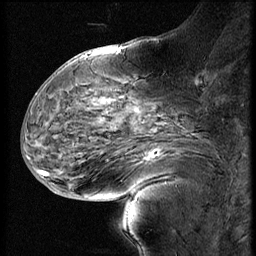
Breast MRI (dynamic contrast-enhanced), one sagittal slice; position 27 of 60 along the scan axis; 4 images stored at this slice position (order not interpretable as contrast timing); 1.5 T; TE 4.2 ms, TR 9 ms; 256 × 256 image matrix. Female patient, age 56 years. From the clinical record (not read from this slice): setting: breast cancer imaged before/during neoadjuvant chemotherapy; receptor status: HER2-positive.
Annotated regions visible in this slice (semi-automatically segmented with operator editing):
- analysis volume of interest (the breast-tissue region the enhancement analysis was run in; not a lesion): bounding box [x1, y1, x2, y2] px = [110, 138, 192, 201]
- tumour enhancement mask (voxels above the 140 % enhancement threshold inside the analysis volume of interest): [146, 153, 154, 161]